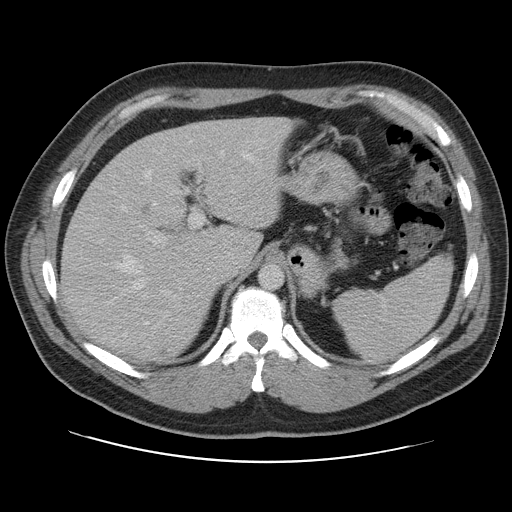
Contrast-enhanced abdominal CT, one axial slice; slice 78 of 109 in the series (ordered by position); soft-tissue window (W 400 / L 40 HU); 5 mm slice thickness; 512 × 512 image matrix. Male patient, age 35 years. From the clinical record (not read from this slice): diagnosis: colorectal cancer liver metastases, imaged before liver resection; multiple liver metastases: yes; largest metastasis: 2.8 cm; disease in both lobes: yes.
Outlined on this slice (manually delineated by an expert):
- hepatic veins: bounding box [x1, y1, x2, y2] px = [104, 151, 260, 325]
- liver: [61, 117, 291, 361]
- planned liver remnant (the part of the liver to remain after resection): [61, 117, 284, 358]
- portal vein (with intrahepatic branches): [97, 160, 211, 299]
- liver metastasis: [161, 350, 169, 356]